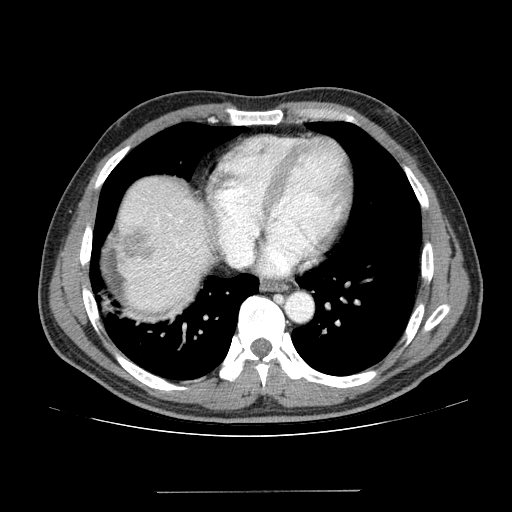
Contrast-enhanced abdominal CT (liver protocol), one axial slice; position 121 of 131 along the scan axis; 100 kVp; one of 2 acquisitions stored at this slice position; soft-tissue window (W 400 / L 40 HU); 512 × 512 image matrix, field of view 380 × 380 mm. Case-level facts recorded for this patient, not image findings: diagnosis: hepatocellular carcinoma (patient treated with transarterial chemoembolisation; whether this scan precedes or follows treatment is not stated here); TNM stage (as recorded): Stage-I; Child-Pugh class: A; tumour differentiation: poorly differentiated; tumour nodularity: uninodular.
Outlined on this slice (semi-automatically segmented with operator editing):
- liver parenchyma outside the tumour (the mass and vessels are separate outlines, so this box may not span the whole liver): box from (x=116, y=176) to (x=210, y=312) px
- mass: (x=105, y=228)–(x=151, y=262)
- liver vessels: (x=131, y=213)–(x=197, y=301)